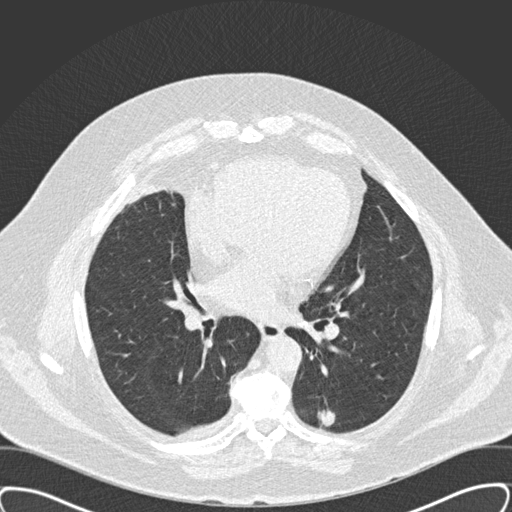
Low-dose screening chest CT, one axial slice; slice 86 of 159 in the series (ordered by position); reconstruction kernel B30f; 120 kVp; lung window (W 1500 / L -600 HU); 2 mm slice thickness; 512 × 512 image matrix, field of view 400 × 400 mm.
Outlined on this slice (expert manual segmentation):
- lesion 1 (tumor, lower lobe of left lung): bounding box (x1, y1, x2, y2) in pixels: (318, 411, 335, 431)